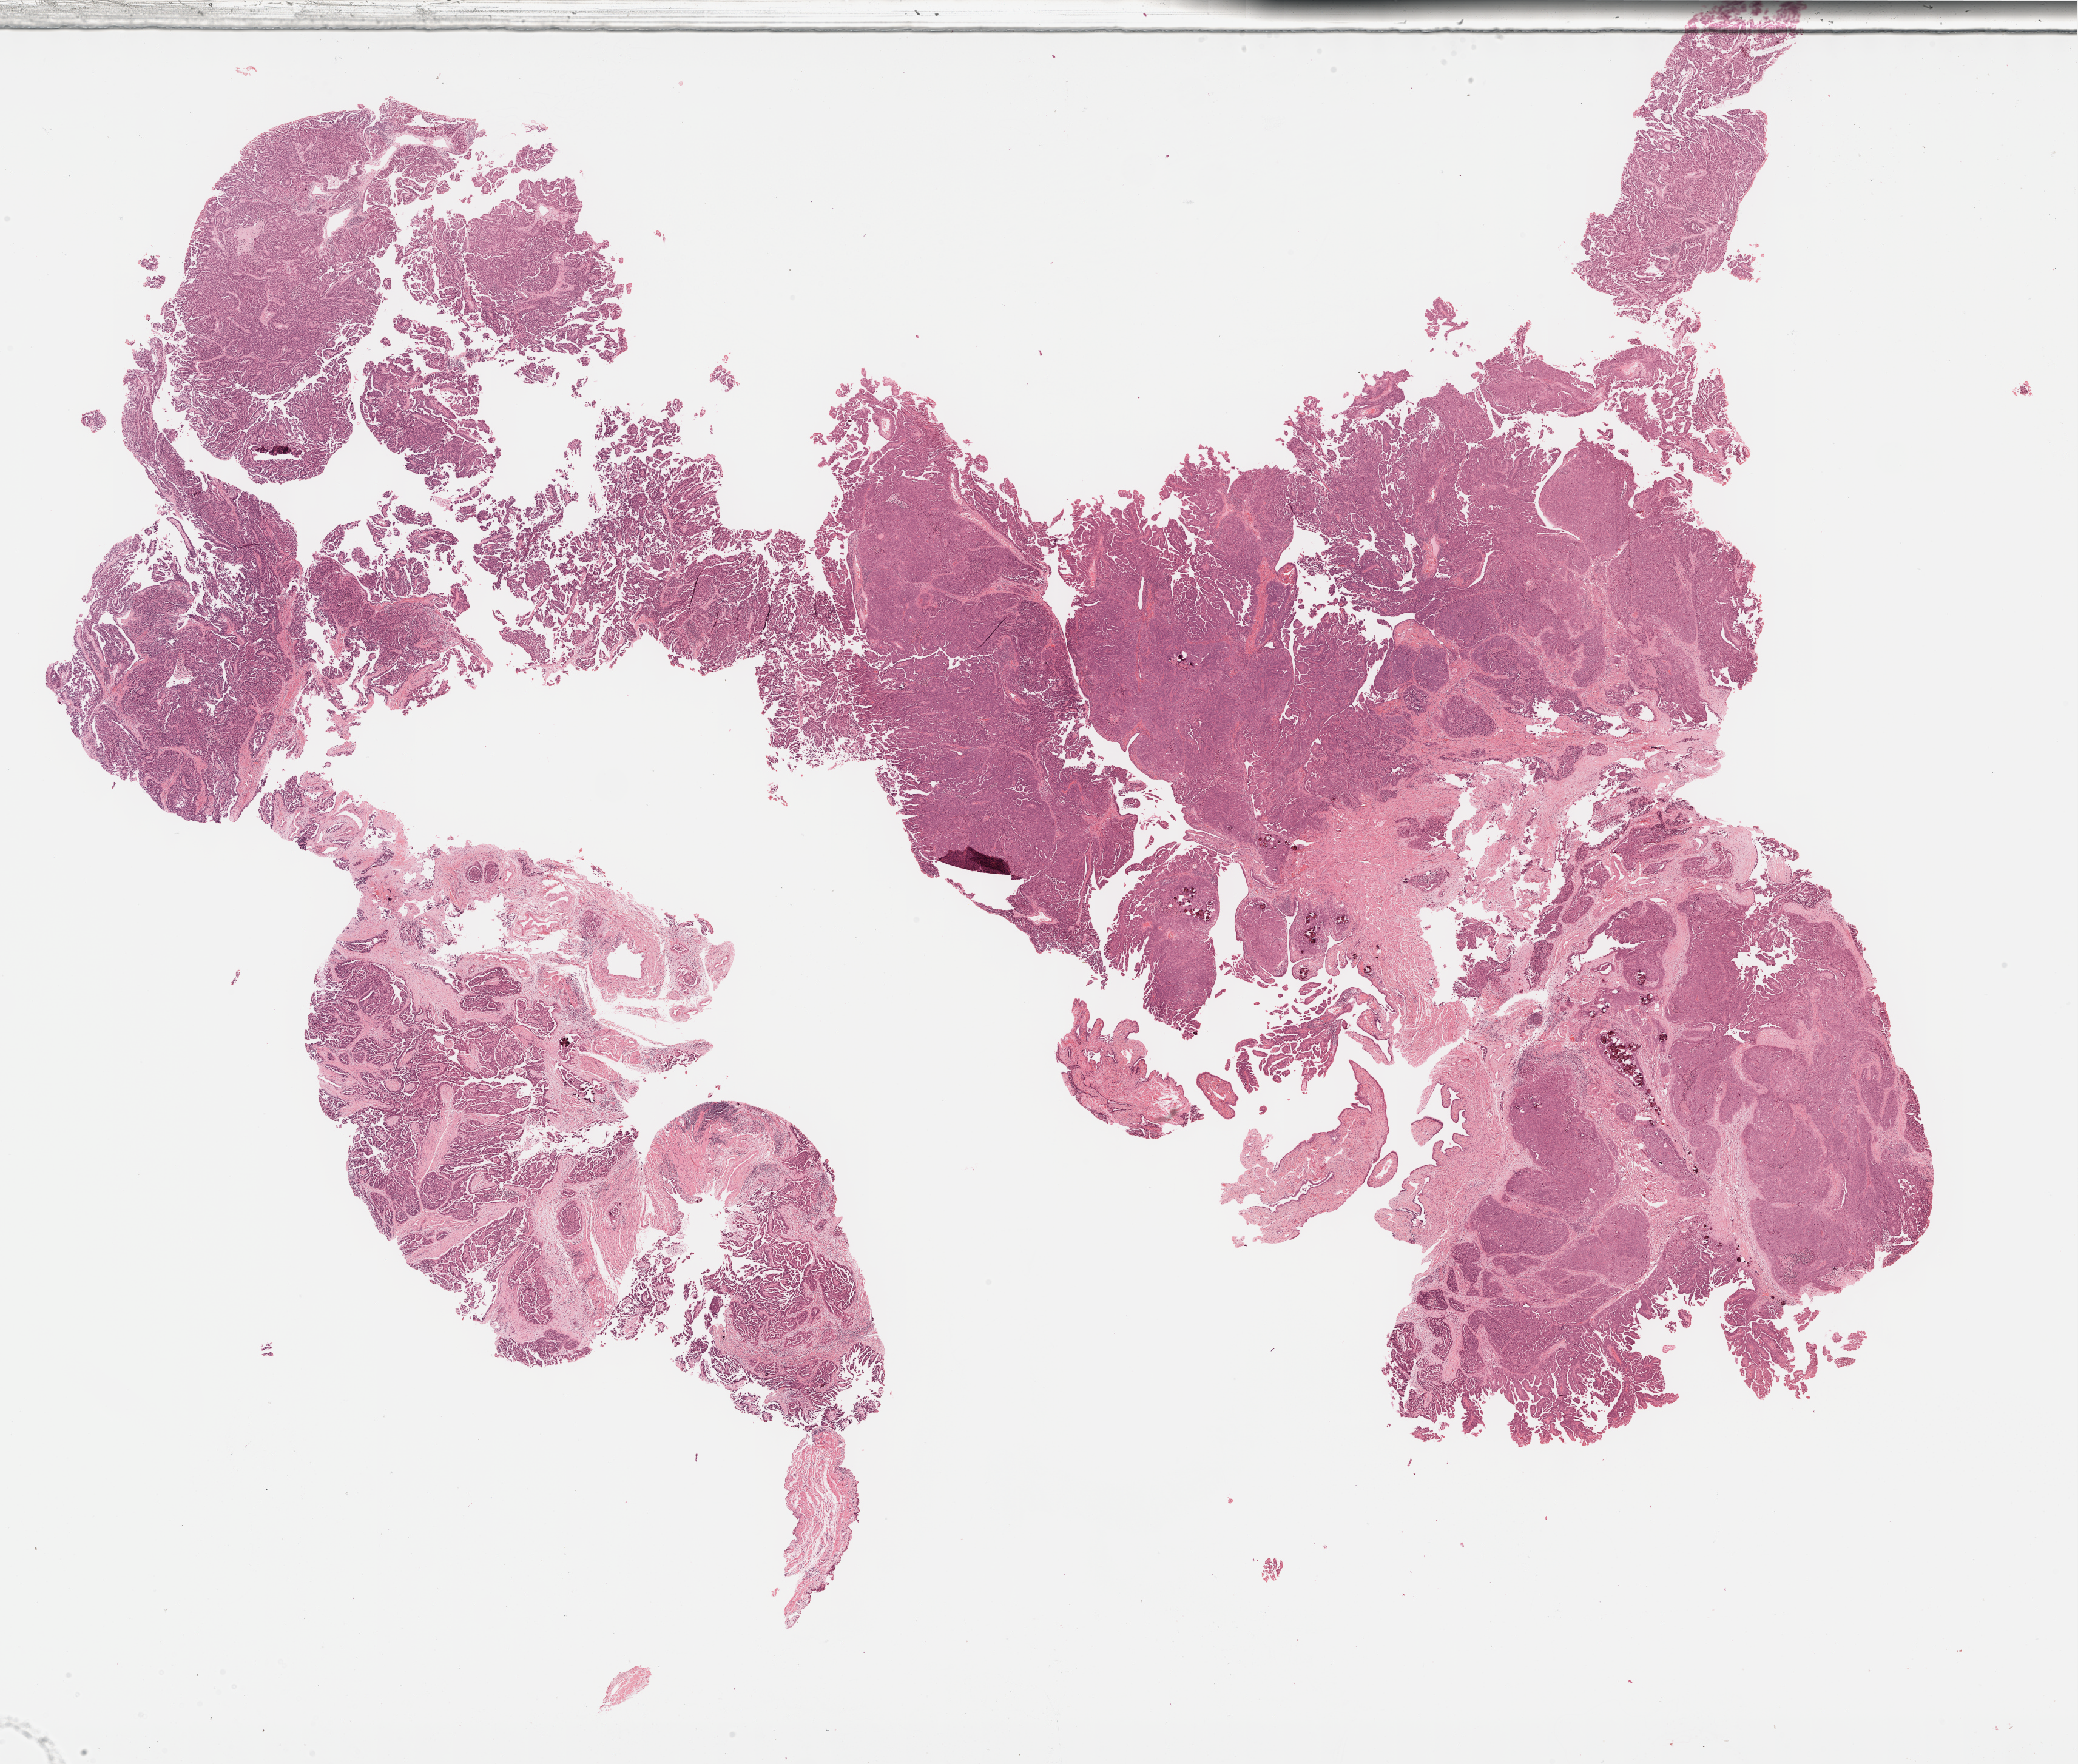
Digitized H&E-stained tissue section (whole slide) — shown as a low-resolution overview of the whole scanned area (about 27.7 x 23.5 mm, acquisition: 40x scan). Formalin-fixed paraffin-embedded (FFPE) diagnostic section. Ovary, primary tumour sample. Female patient; age at initial diagnosis 74 years. Histologic grade: G3 (poorly differentiated).
Diagnosis: Serous cystadenocarcinoma, NOS. FIGO stage: IIIC.